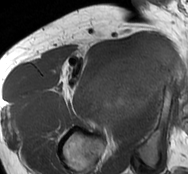
MRI of an extremity soft-tissue mass, one axial slice; slice 64 of 93 in the series (ordered by position); MR volume resampled by the dataset authors to the PET/CT grid (not the native acquisition matrix); 3.27 mm slice thickness; 188 × 174 image matrix, field of view 184 × 170 mm. Male patient. From the clinical record (not read from this slice): histological type: undifferentiated - pleiomorphic; grade: high; site of the primary tumour: right thigh.
Structures marked on this image (expert contour drawn on MRI and transferred to this co-registered scan by the dataset authors):
- gross tumour volume including surrounding oedema: box from (x=90, y=35) to (x=180, y=127) px
- gross tumour volume (mass): (x=90, y=39)–(x=178, y=127)